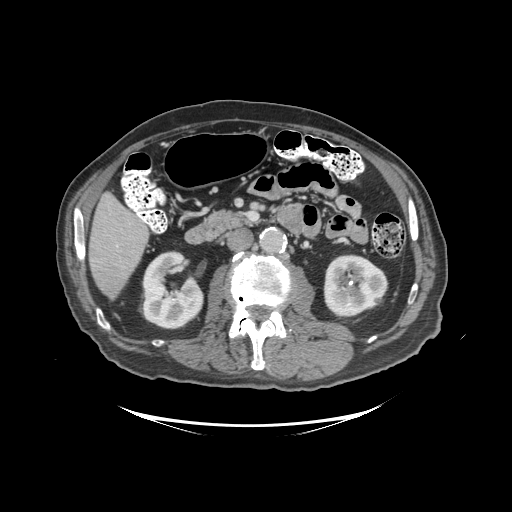
Contrast-enhanced abdominal CT (liver protocol), one axial slice. Slice 37 of 99 in the series (ordered by position). Reconstruction kernel STANDARD. 140 kVp. Soft-tissue window (W 400 / L 40 HU). 2.5 mm slice thickness. 512 × 512 image matrix, field of view 460 × 460 mm. From the clinical record (not read from this slice): diagnosis: hepatocellular carcinoma (patient treated with transarterial chemoembolisation; whether this scan precedes or follows treatment is not stated here); TNM stage (as recorded): Stage-I.
Structures marked on this image (semi-automatically segmented with operator editing):
- liver parenchyma outside the tumour (the mass and vessels are separate outlines, so this box may not span the whole liver): bounding box <88,192,148,300> (left, top, right, bottom; pixels)
- mass: <96,266,125,295>